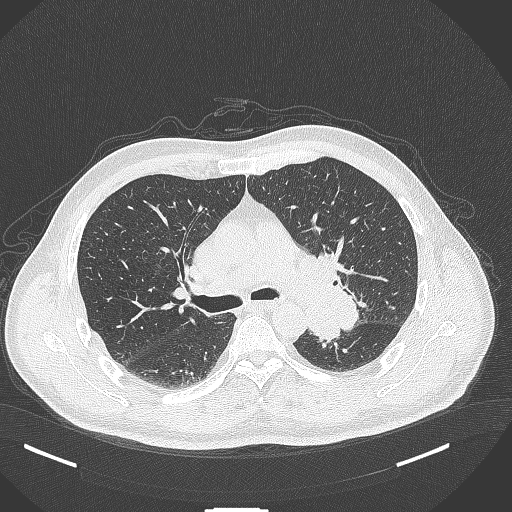
Chest CT, one axial slice. Position 260 of 429 along the scan axis. 120 kVp. Lung window (W 1500 / L -600 HU). 1 mm slice thickness. 512 × 512 image matrix, field of view 400 × 400 mm. Male patient, age 55 years. From the clinical record (not read from this slice): clinical TNM (as recorded): T3 N0 M1c.
Outlined on this slice (rectangle marked by the reading radiologist):
- lung tumour (recorded histology: adenocarcinoma): bounding box [x1, y1, x2, y2] px = [305, 288, 367, 348]